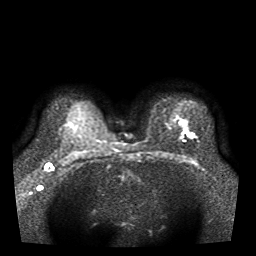
Breast MRI, one axial slice. Diffusion-weighted series; image 2 of 4 stored at this slice position (different b-values; order by instance number). 1.5 T. 5 mm slice thickness. 256 × 256 image matrix, field of view 330 × 330 mm. Female patient.
Structures marked on this image (manually delineated by an expert):
- tumour on diffusion-weighted imaging: box from (x=191, y=134) to (x=195, y=138) px